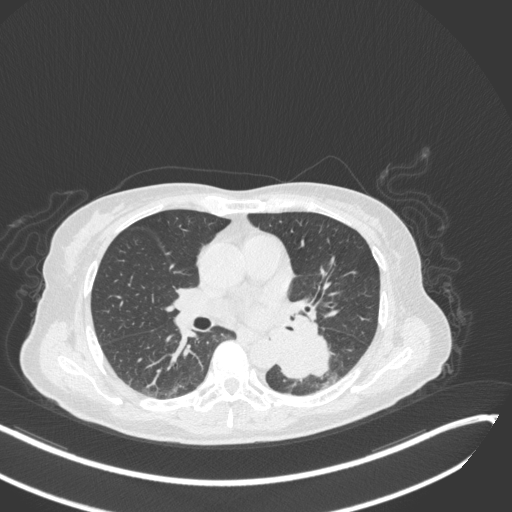
Chest CT, one axial slice; slice 146 of 342 in the series (ordered by position); lung window (W 1500 / L -600 HU); 1 mm slice thickness; 512 × 512 image matrix, field of view 400 × 400 mm. Patient: female, 64 years. Case-level facts recorded for this patient, not image findings: clinical TNM (as recorded): T3 N1 M1.
Annotated regions visible in this slice (rectangle marked by the reading radiologist):
- lung tumour (recorded histology: small cell carcinoma): bounding box (x1, y1, x2, y2) in pixels: (273, 331, 332, 381)